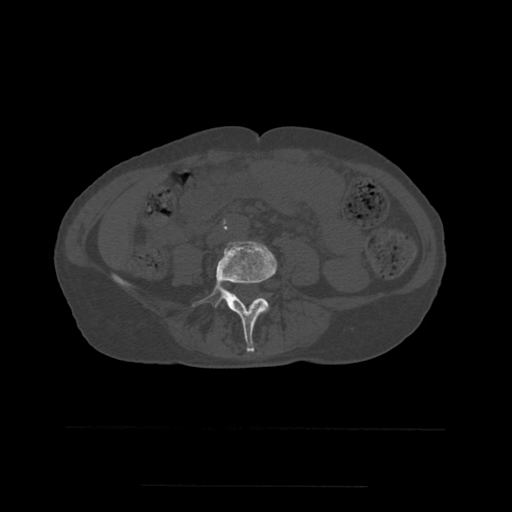
CT including the spine, one axial slice. Slice 164 of 544 in the series (ordered by position). Bone window (W 1800 / L 400 HU). 1.25 mm slice thickness. 512 × 512 image matrix, field of view 350 × 350 mm. Patient age 58 years. Case-level facts recorded for this patient, not image findings: primary cancer: lung.
Outlined on this slice (semi-automatic segmentation, software-assisted and operator-edited):
- L4 vertebra: bounding box [x1, y1, x2, y2] px = [193, 241, 277, 353]
- L5 vertebra: [231, 294, 236, 296]